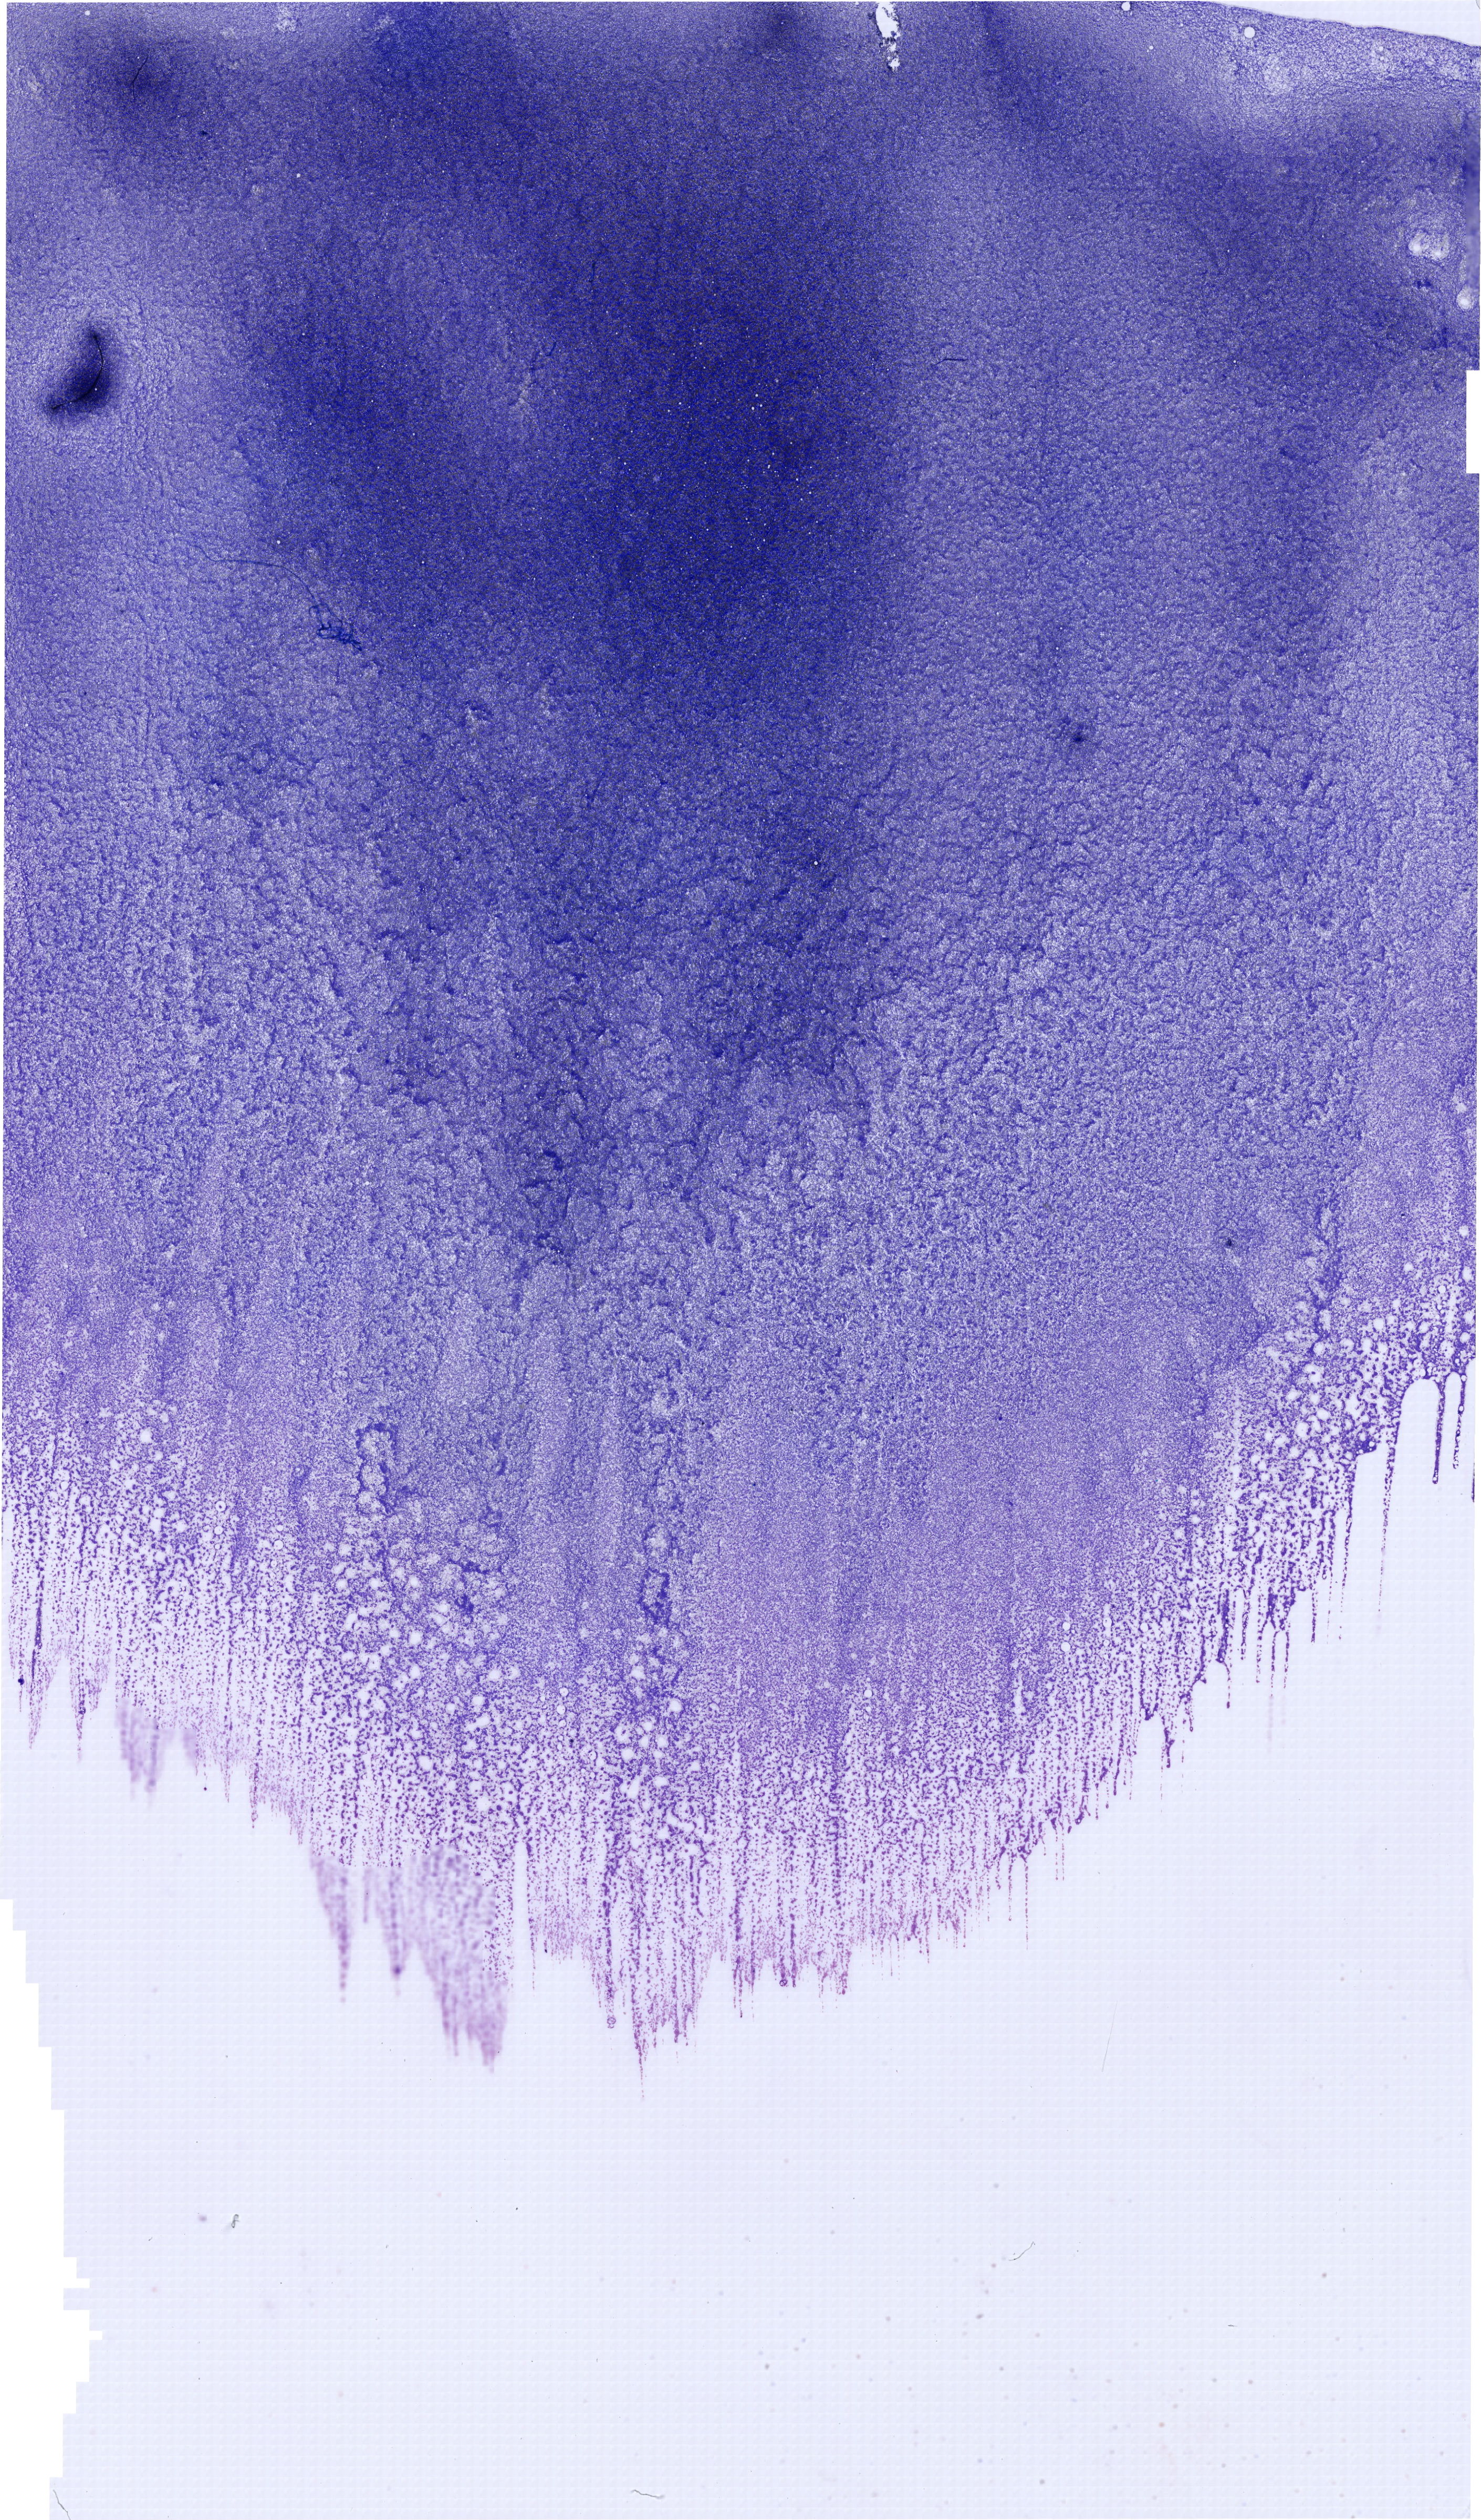
Whole-slide image of a May-Grünwald-Giemsa (MGG)-stained bone marrow aspirate smear, a low-resolution overview of the entire scanned area, about 22.0 x 37.5 mm. Patient sex: male.
Diagnosis: T Acute Lymphoblastic Leukemia.